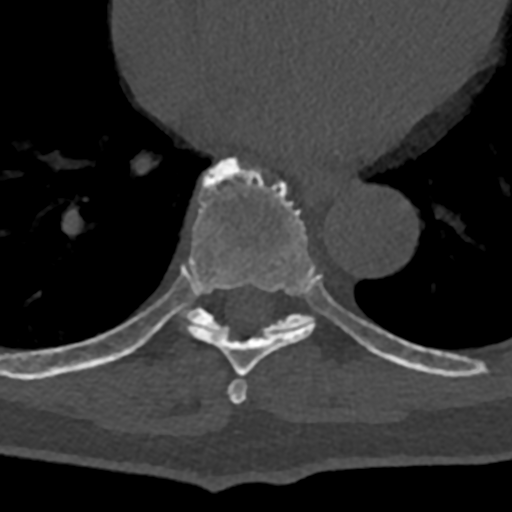
CT including the spine, one axial slice; position 693 of 797 along the scan axis; reconstruction kernel Br40s/3; 120 kVp; bone window (W 1800 / L 400 HU); 512 × 512 image matrix. Male patient, age 74 years. Case-level facts recorded for this patient, not image findings: primary cancer: renal.
Structures marked on this image (semi-automatically segmented with operator editing):
- T7 vertebra: bounding box <228,379,247,404> (left, top, right, bottom; pixels)
- T8 vertebra: <70,157,391,376>
- T9 vertebra: <110,268,432,374>